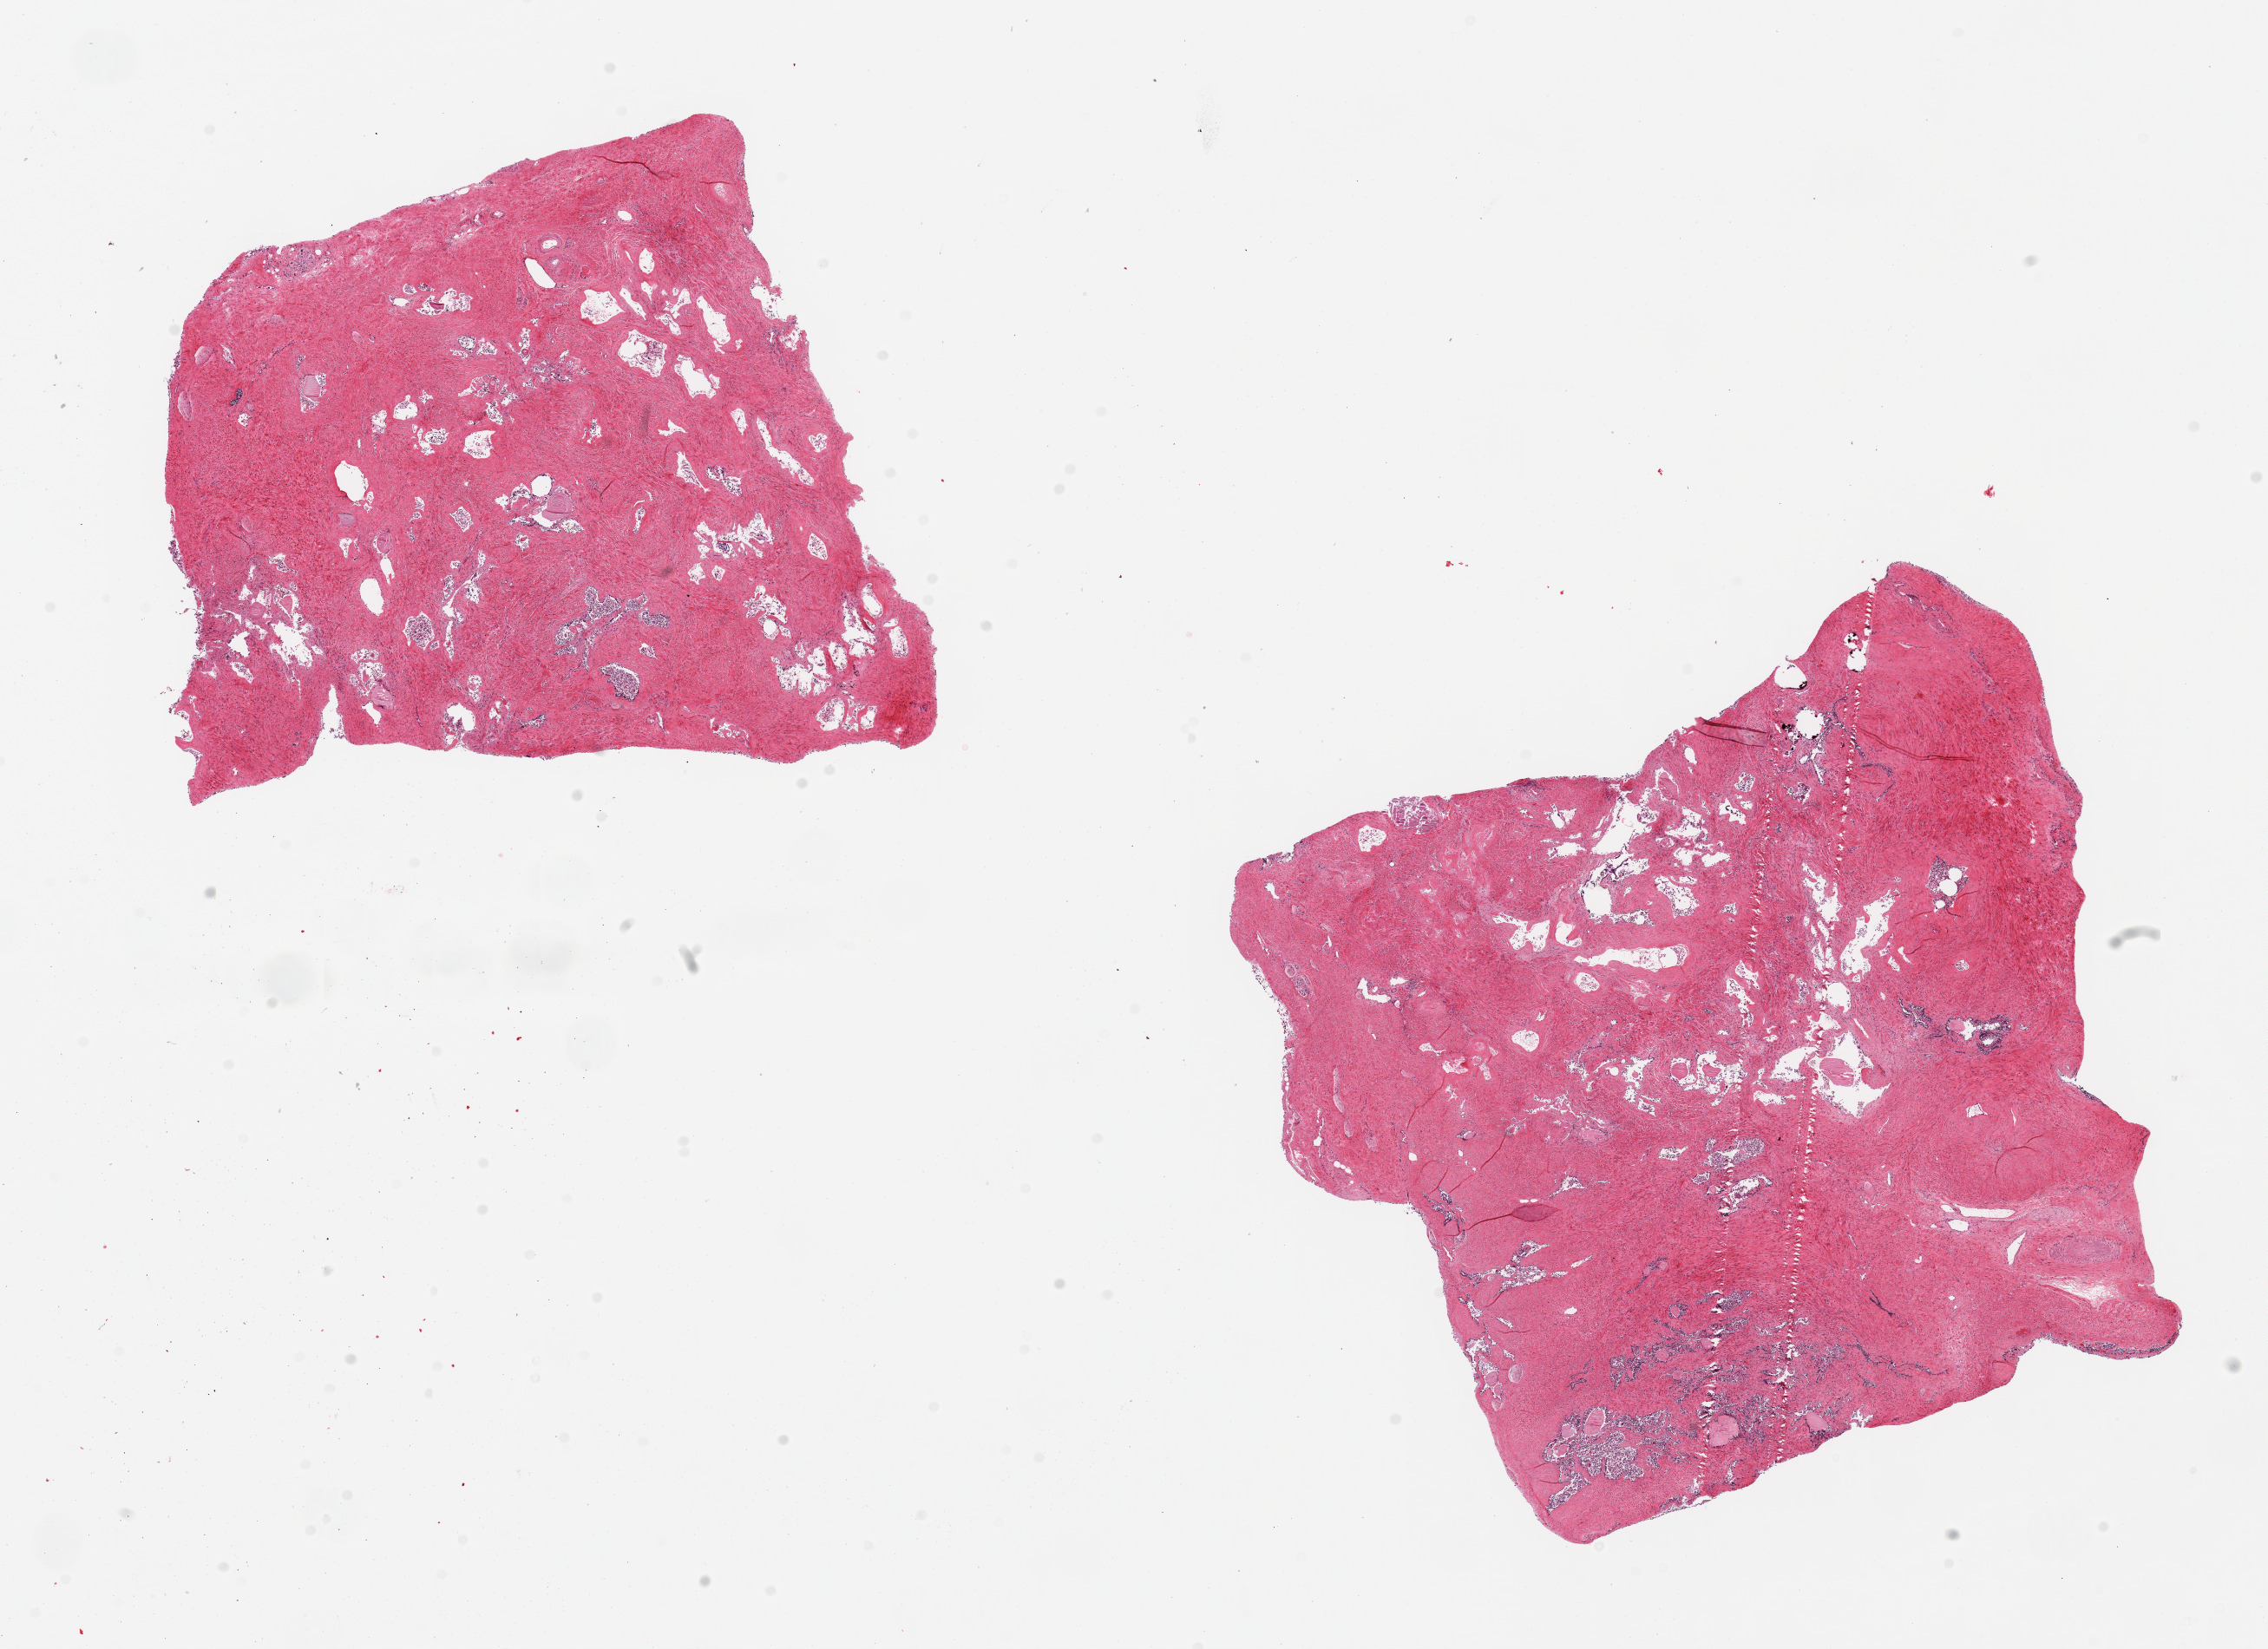
Whole-slide image, haematoxylin and eosin stain, brightfield, a low-resolution overview of the entire scanned area, about 20.7 x 15.0 mm (acquisition: 20x scan). PAXgene-fixed, paraffin-embedded tissue. Section of prostate (target tissue). Tissue donor sample. Donor sex: male.
Reviewer comment on this tissue sample: 2 pieces, 7x6 & 8x8mm; Glands = 3; stroma = 2.